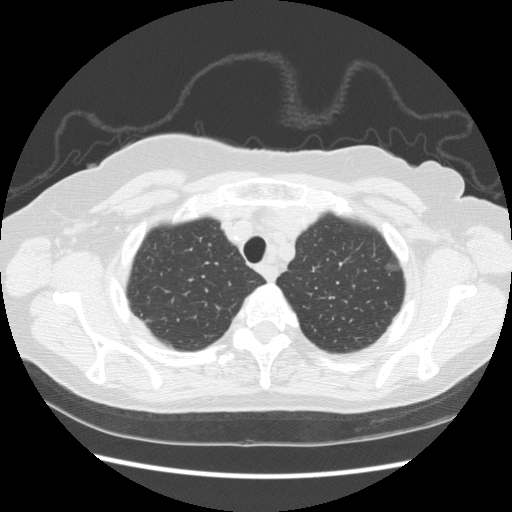
Axial slice from a low-dose chest CT screening exam, baseline annual screen, lung window (W 1500 / L -600 HU), 2.5 mm slice thickness, standard (soft-tissue) reconstruction kernel (STANDARD), 512 × 512 image matrix, field of view 360 × 360 mm. Female, age 73 years at enrolment.
Expert-annotated lung lesion, bounding box [x1, y1, x2, y2] px = [370, 233, 411, 282]. The screening reader recorded 3 non-calcified nodules or masses ≥4 mm on this exam (left upper lobe, left upper lobe, left upper lobe); which of them this box marks is not recorded.